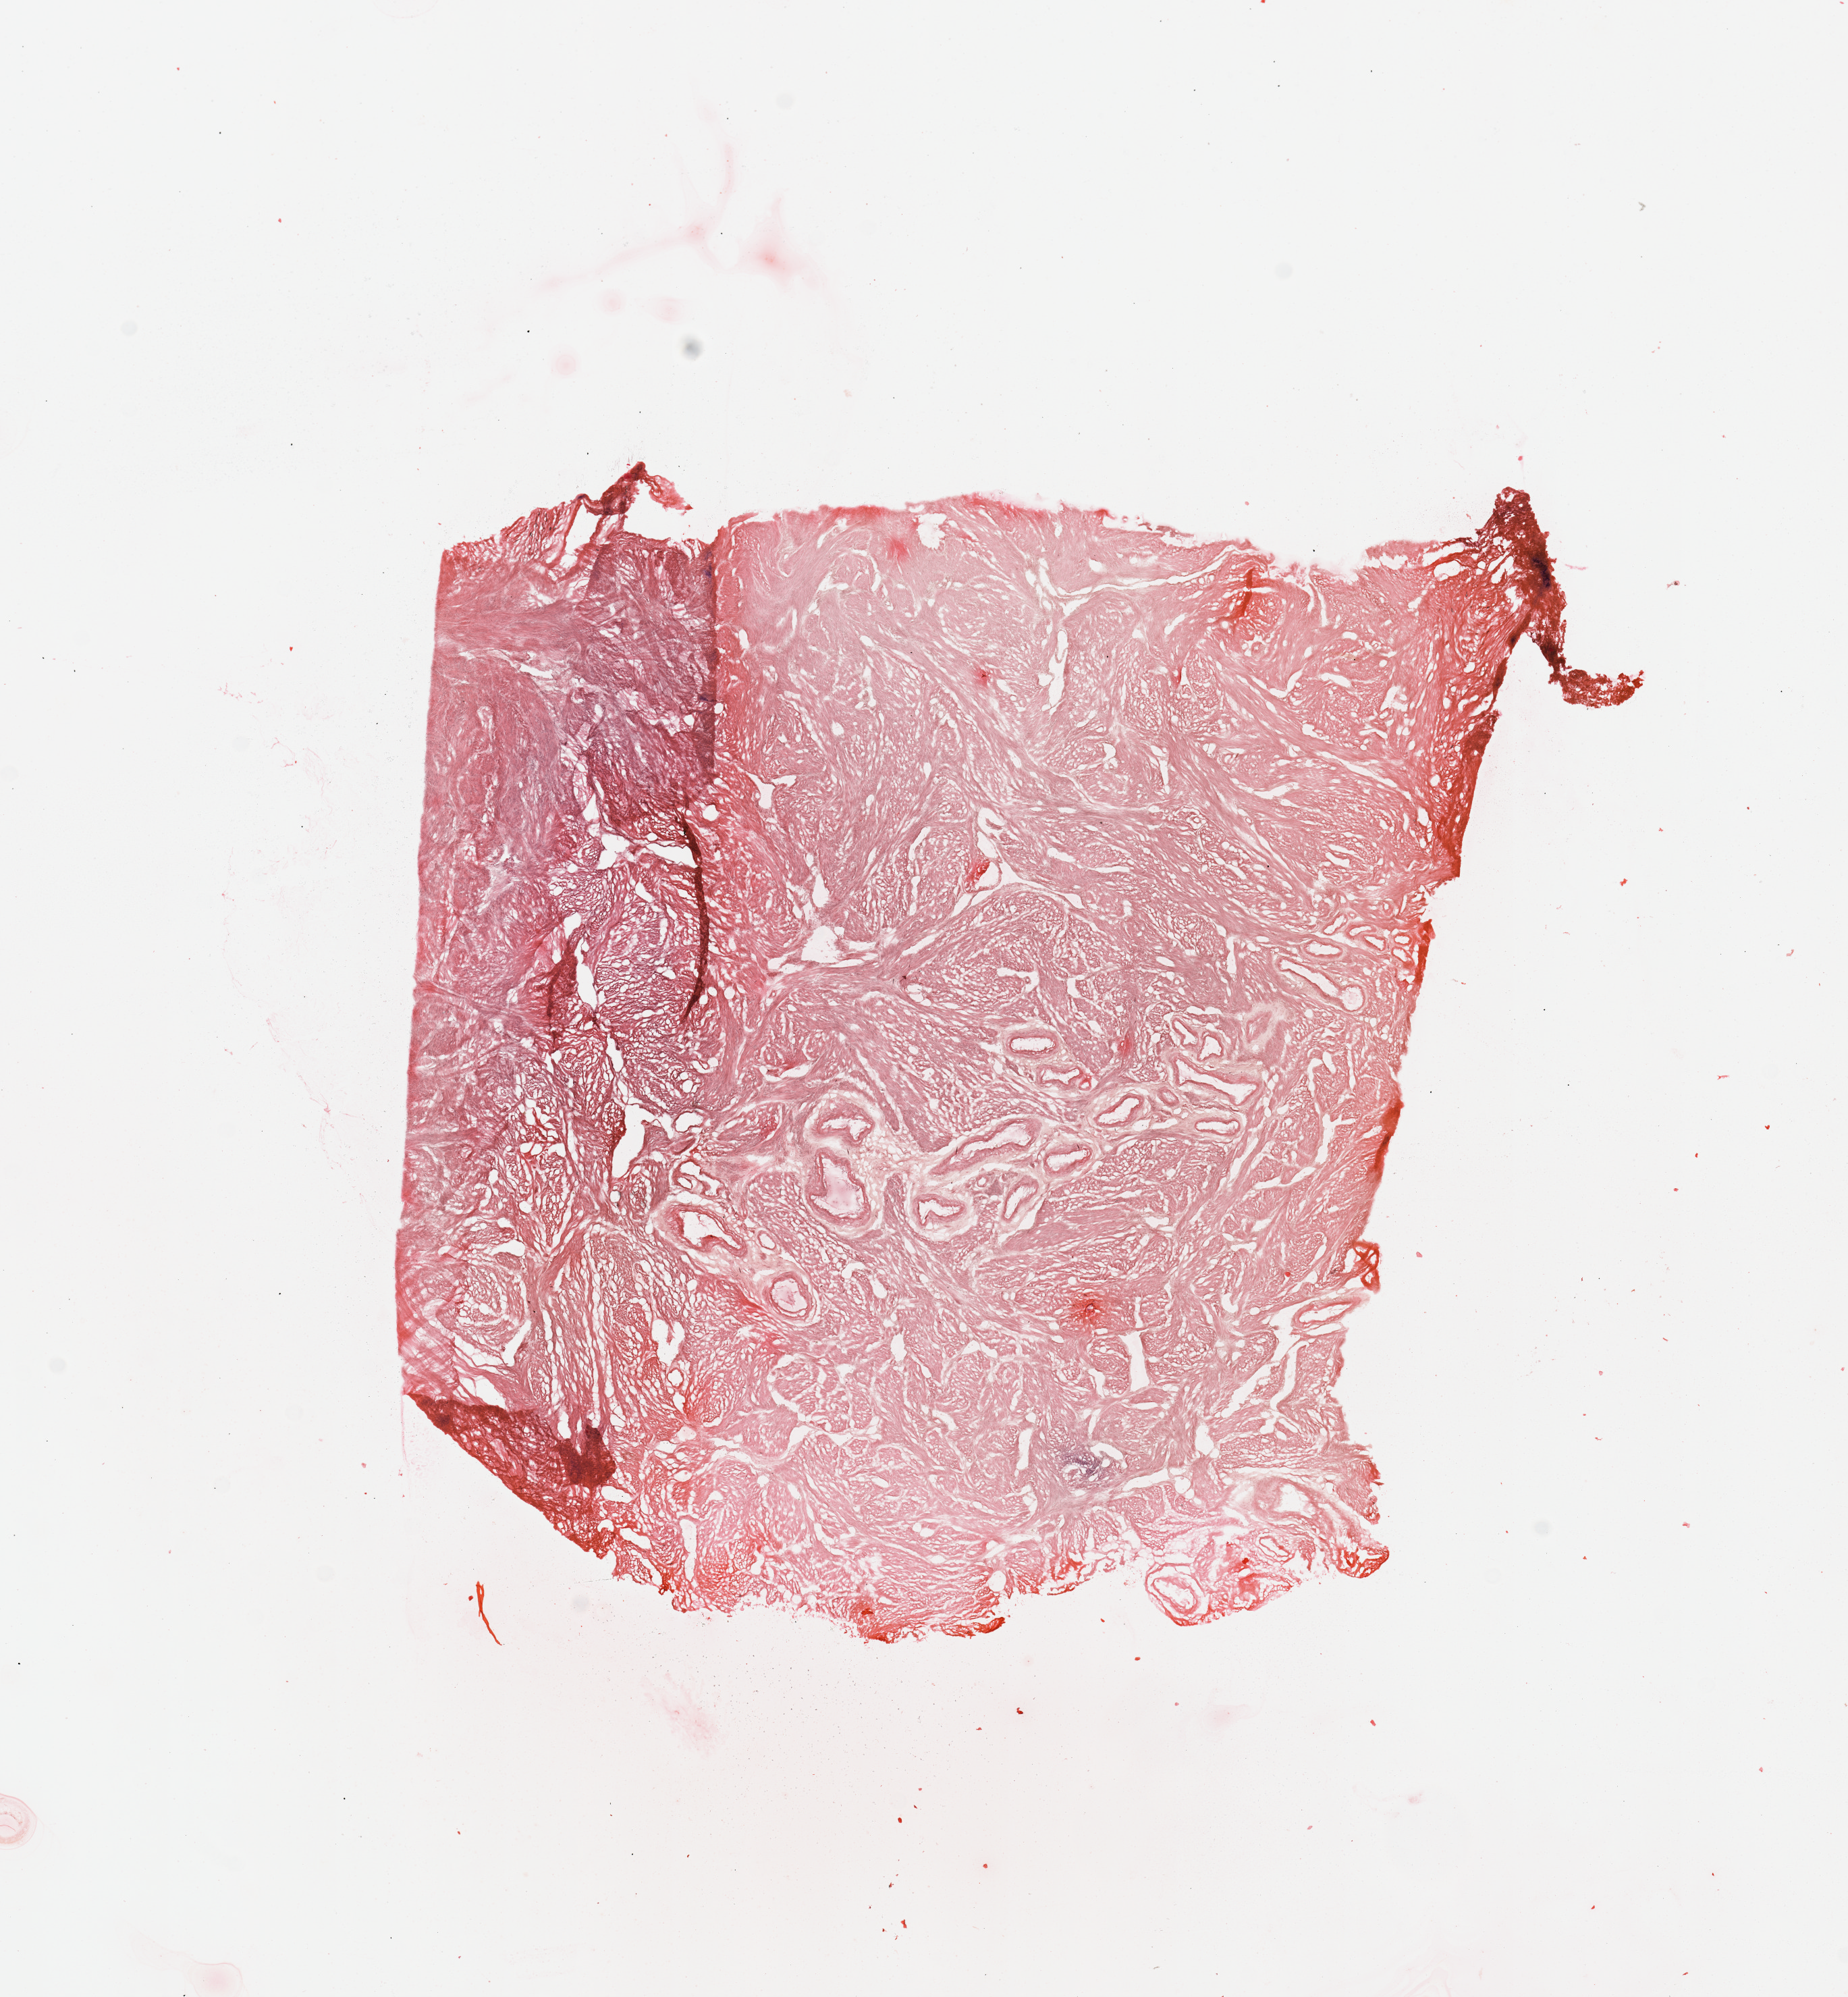
Whole-slide histology image, H&E-stained — shown as a low-resolution overview of the whole scanned area (about 10.8 x 11.7 mm, slide scanned at 20x); uterus, normal (non-tumour) tissue. 61-year-old female patient.
This section: normal (non-tumour) tissue from the same patient. Patient diagnosis: Endometrioid adenocarcinoma, NOS.